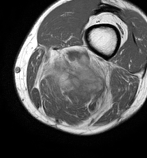
MRI of an extremity soft-tissue mass, one axial slice; MR volume resampled by the dataset authors to the PET/CT grid (not the native acquisition matrix); 3.27 mm slice thickness; 147 × 158 image matrix. Male patient. Case-level facts recorded for this patient, not image findings: histological type: undifferentiated pleomorphic liposarcoma; grade: high; site of the primary tumour: left thigh.
Annotated regions visible in this slice (expert contour drawn on MRI and transferred to this co-registered scan by the dataset authors):
- gross tumour volume including surrounding oedema: bounding box [x1, y1, x2, y2] px = [34, 44, 115, 123]
- gross tumour volume (mass): [73, 83, 86, 93]